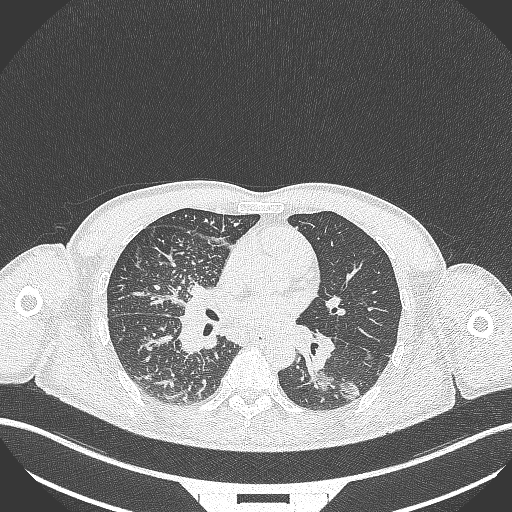
Chest CT, one axial slice. Reconstruction kernel B70f. 120 kVp. Lung window (W 1500 / L -600 HU). 1 mm slice thickness. 512 × 512 image matrix, field of view 400 × 400 mm. Male patient, age 49 years. Case-level facts recorded for this patient, not image findings: clinical TNM (as recorded): T2b N1 M0.
Annotated regions visible in this slice (bounding box drawn by a radiologist):
- lung tumour (recorded histology: adenocarcinoma): bounding box [x1, y1, x2, y2] px = [306, 364, 364, 405]